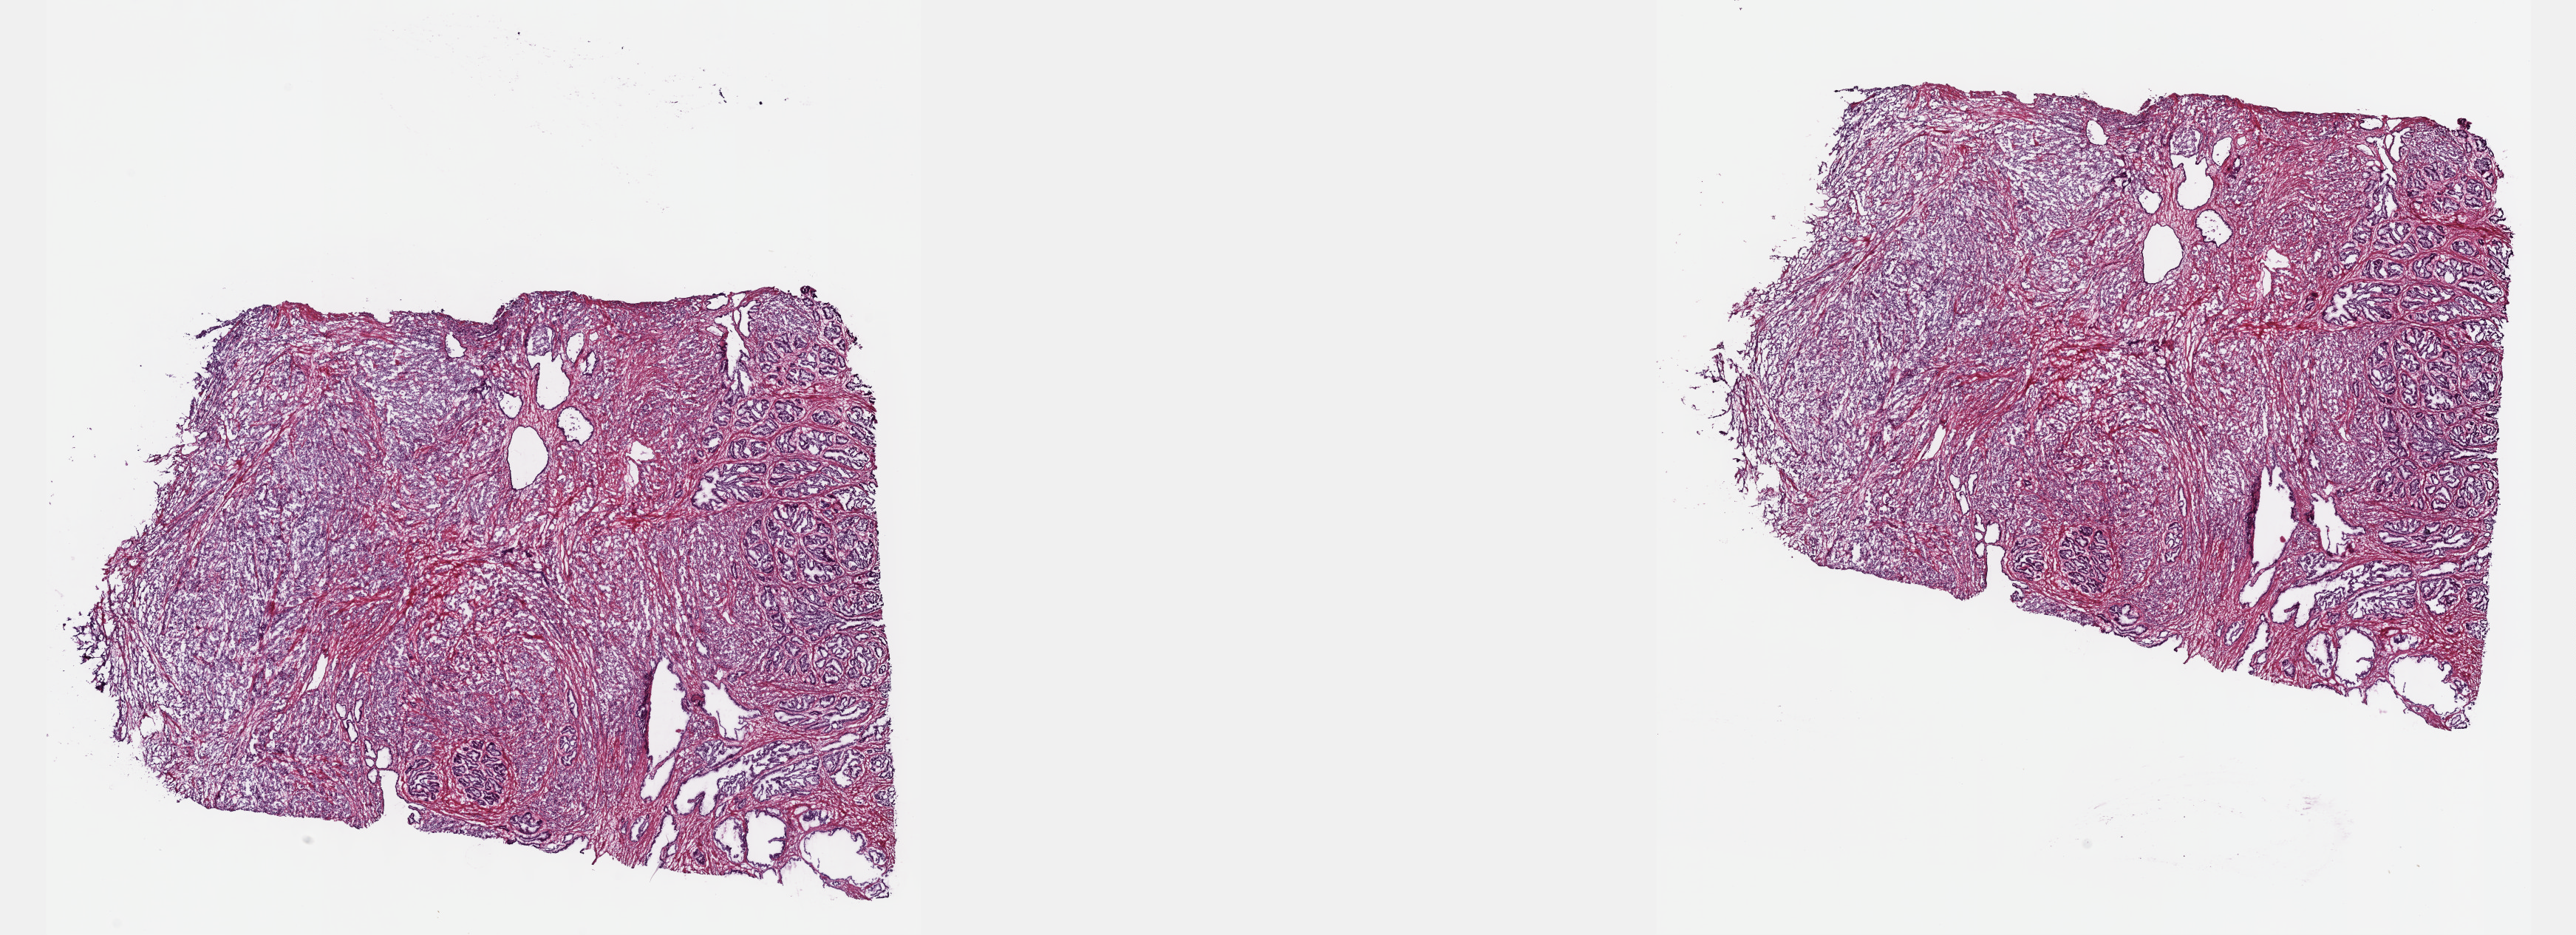
Whole-slide histology image, H&E — a low-resolution overview of the entire scanned area, about 28.2 x 10.2 mm (slide scanned at 40x), frozen section, primary tumour sample from the prostate. Male patient; age at initial diagnosis 64 years. Gleason score: 9 (5+4). Pathologist review of this section (percent, as recorded): tumour cells 70%, tumour nuclei 80%, normal cells 10%, stromal cells 20%, necrosis 0%. Infiltration values recorded for this section: lymphocyte infiltration 0%, monocyte infiltration 0%, neutrophil infiltration 0%.
Pathologic diagnosis: Adenocarcinoma, NOS (prostate gland). Lymph nodes positive (case pathology): 0 of 25 examined. Laterality: bilateral.